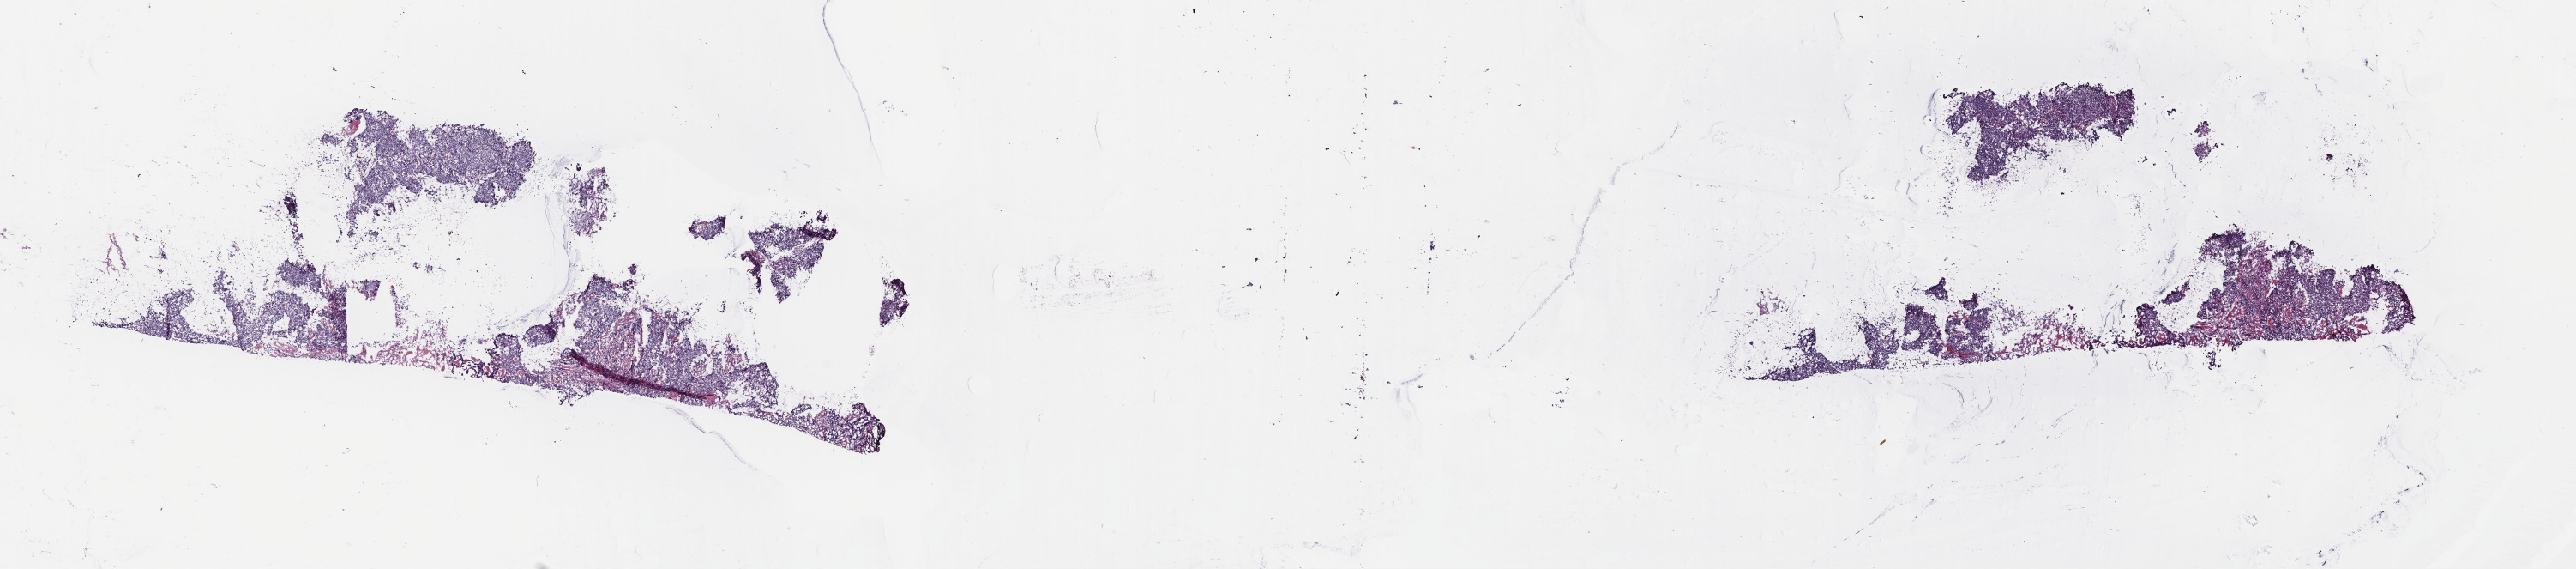
Whole-slide histology image, H&E — shown as a low-resolution overview of the whole scanned area (about 23.6 x 5.2 mm); frozen section; breast, primary tumour sample. Female patient; age at initial diagnosis 52 years. Composition of this section per pathologist review: tumour cells 75%, tumour nuclei 95%, normal cells 0%, stromal cells 10%, necrosis 15%. Inflammatory infiltration, as recorded: lymphocyte infiltration 1%, monocyte infiltration 0%, neutrophil infiltration 0%.
Pathologic diagnosis: Infiltrating duct carcinoma, NOS. Lymph nodes positive (case pathology): 0 of 6 examined. AJCC pathologic stage: IIA.